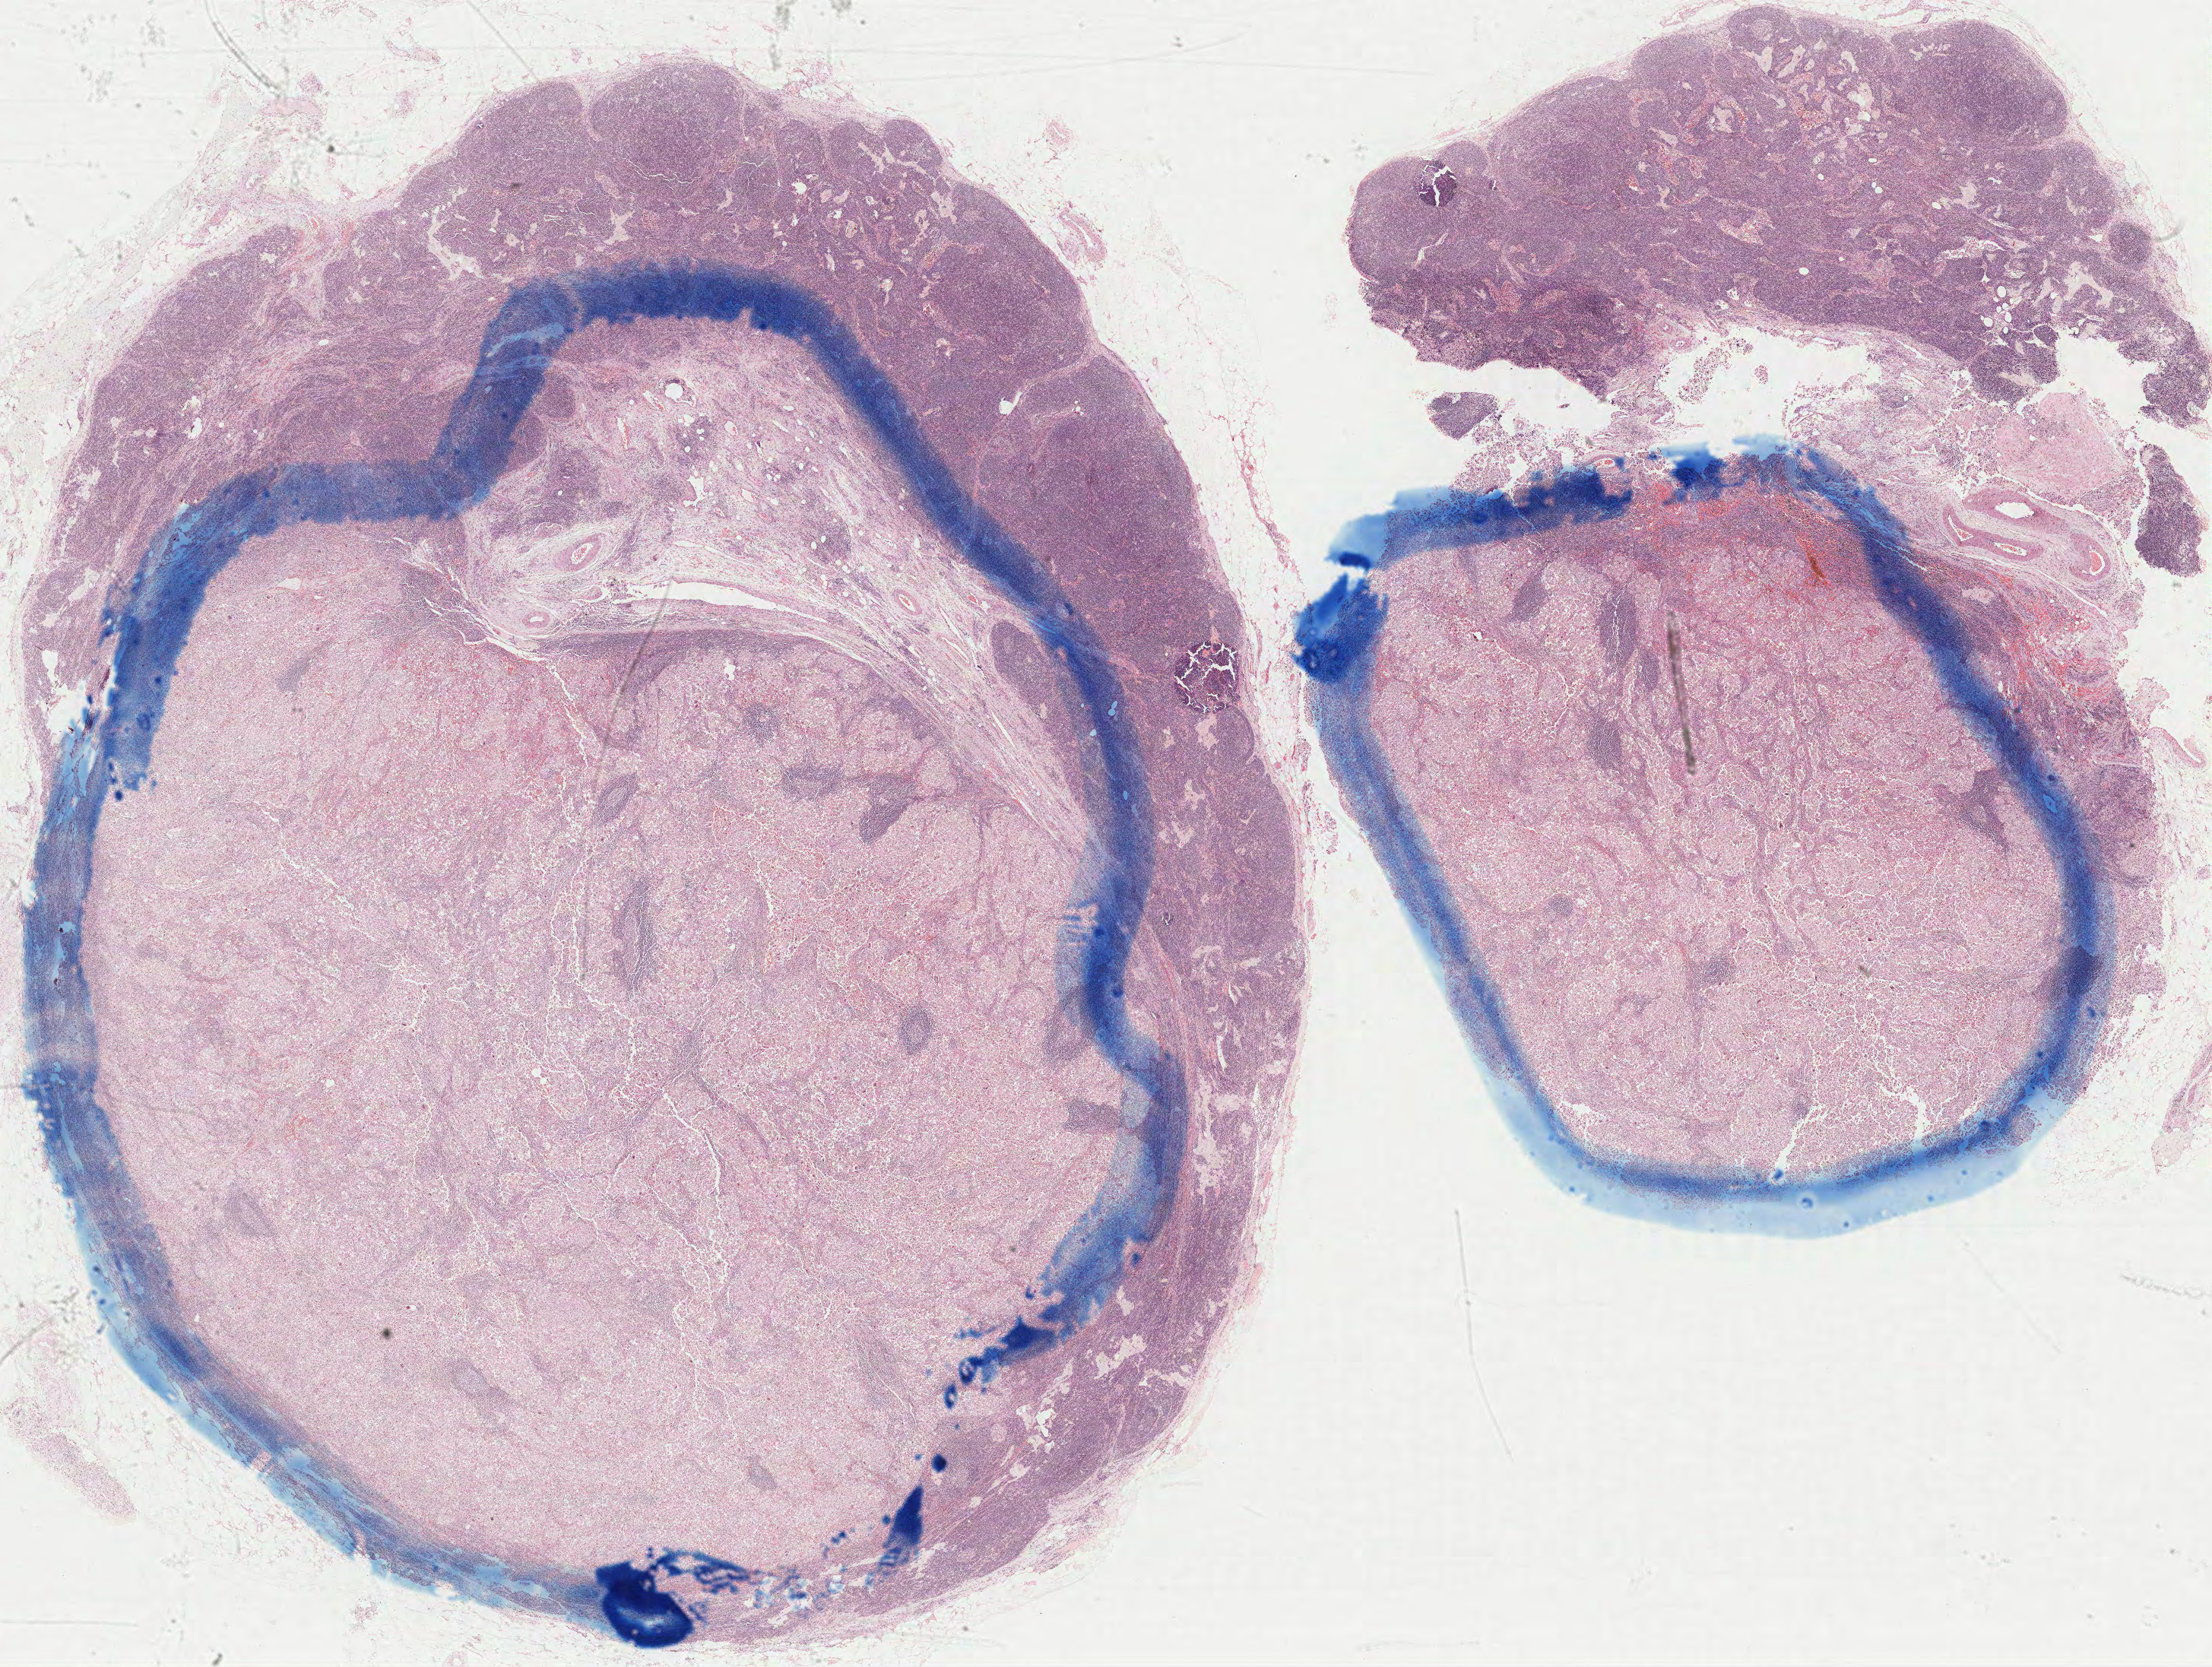
H&E whole-slide image, shown as a low-resolution overview of the whole scanned area (about 23.3 x 17.6 mm, slide scanned at 40x), formalin-fixed paraffin-embedded (FFPE) diagnostic section, metastatic tumour sample, sampled site not recorded. Male patient; age at initial diagnosis 48 years.
* this section: metastatic tumour tissue
* patient diagnosis: Malignant melanoma, NOS